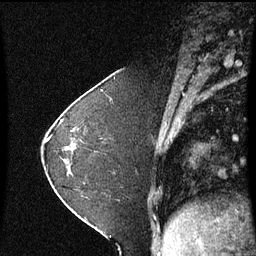
Breast MRI (dynamic contrast-enhanced), one sagittal slice. Position 20 of 60 along the scan axis. Dynamic contrast-enhanced series, image 2 of 3 at this slice position (ordered by acquisition). 1.5 T. TE 4.2 ms, TR 8.9 ms. 2 mm slice thickness. 256 × 256 image matrix. Female patient, age 37 years. From the clinical record (not read from this slice): setting: breast cancer imaged before/during neoadjuvant chemotherapy; receptor status: HR-positive, HER2-negative.
Structures marked on this image (semi-automatically segmented with operator editing):
- analysis volume of interest (the breast-tissue region the enhancement analysis was run in; not a lesion): box from (x=60, y=102) to (x=122, y=181) px
- tumour enhancement mask (voxels above the 70 % enhancement threshold inside the analysis volume of interest): (x=61, y=120)–(x=73, y=133)